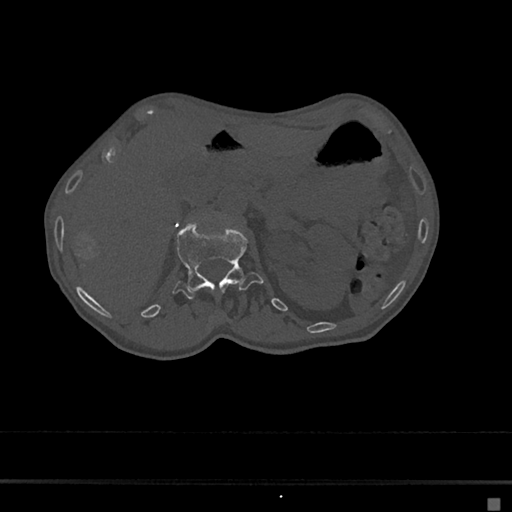
CT including the spine, one axial slice. Position 73 of 797 along the scan axis. Reconstruction kernel Br40s/3. Bone window (W 1800 / L 400 HU). 0.5 mm slice thickness. 512 × 512 image matrix. Patient: female, 68 years. Case-level facts recorded for this patient, not image findings: primary cancer: renal.
Annotated regions visible in this slice (semi-automatically segmented with operator editing):
- L1 vertebra: bounding box [x1, y1, x2, y2] px = [172, 220, 264, 299]